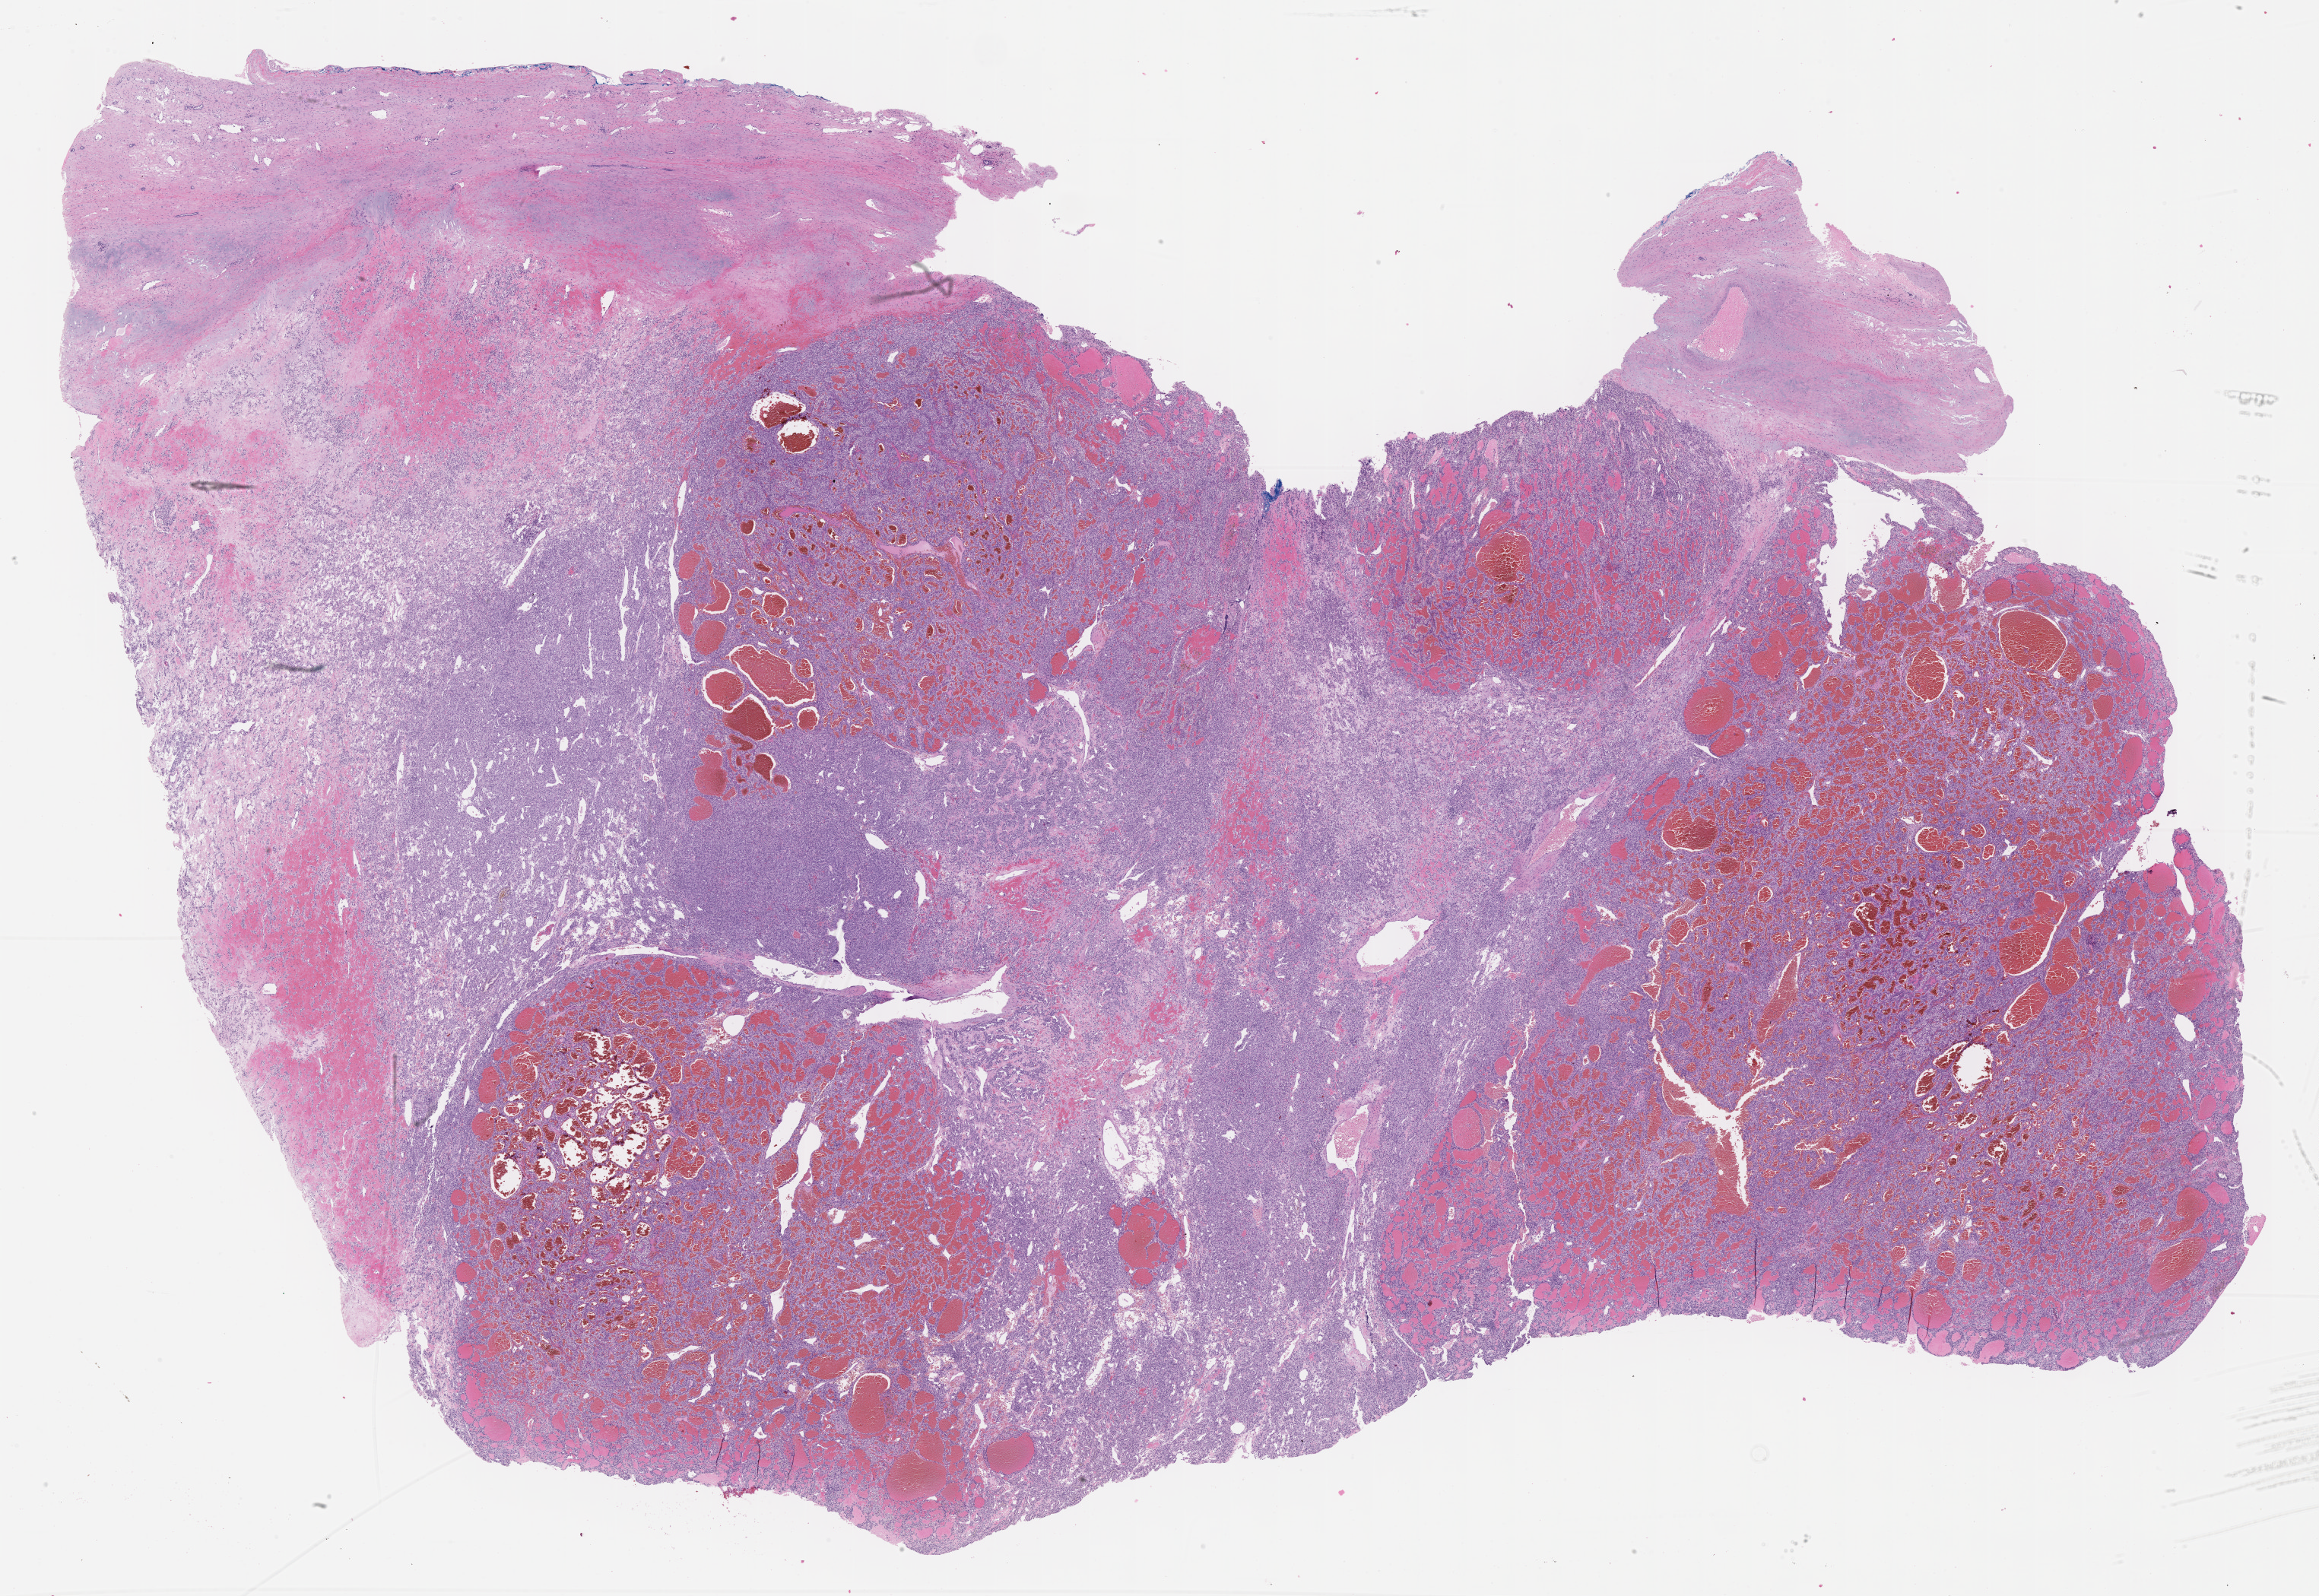
Whole-slide histology image, H&E, a low-resolution overview of the entire scanned area, about 24.7 x 17.0 mm, FFPE section, primary tumour sample from the kidney. Male patient; age at initial diagnosis 58 years.
Histologic diagnosis: Clear cell adenocarcinoma, NOS.